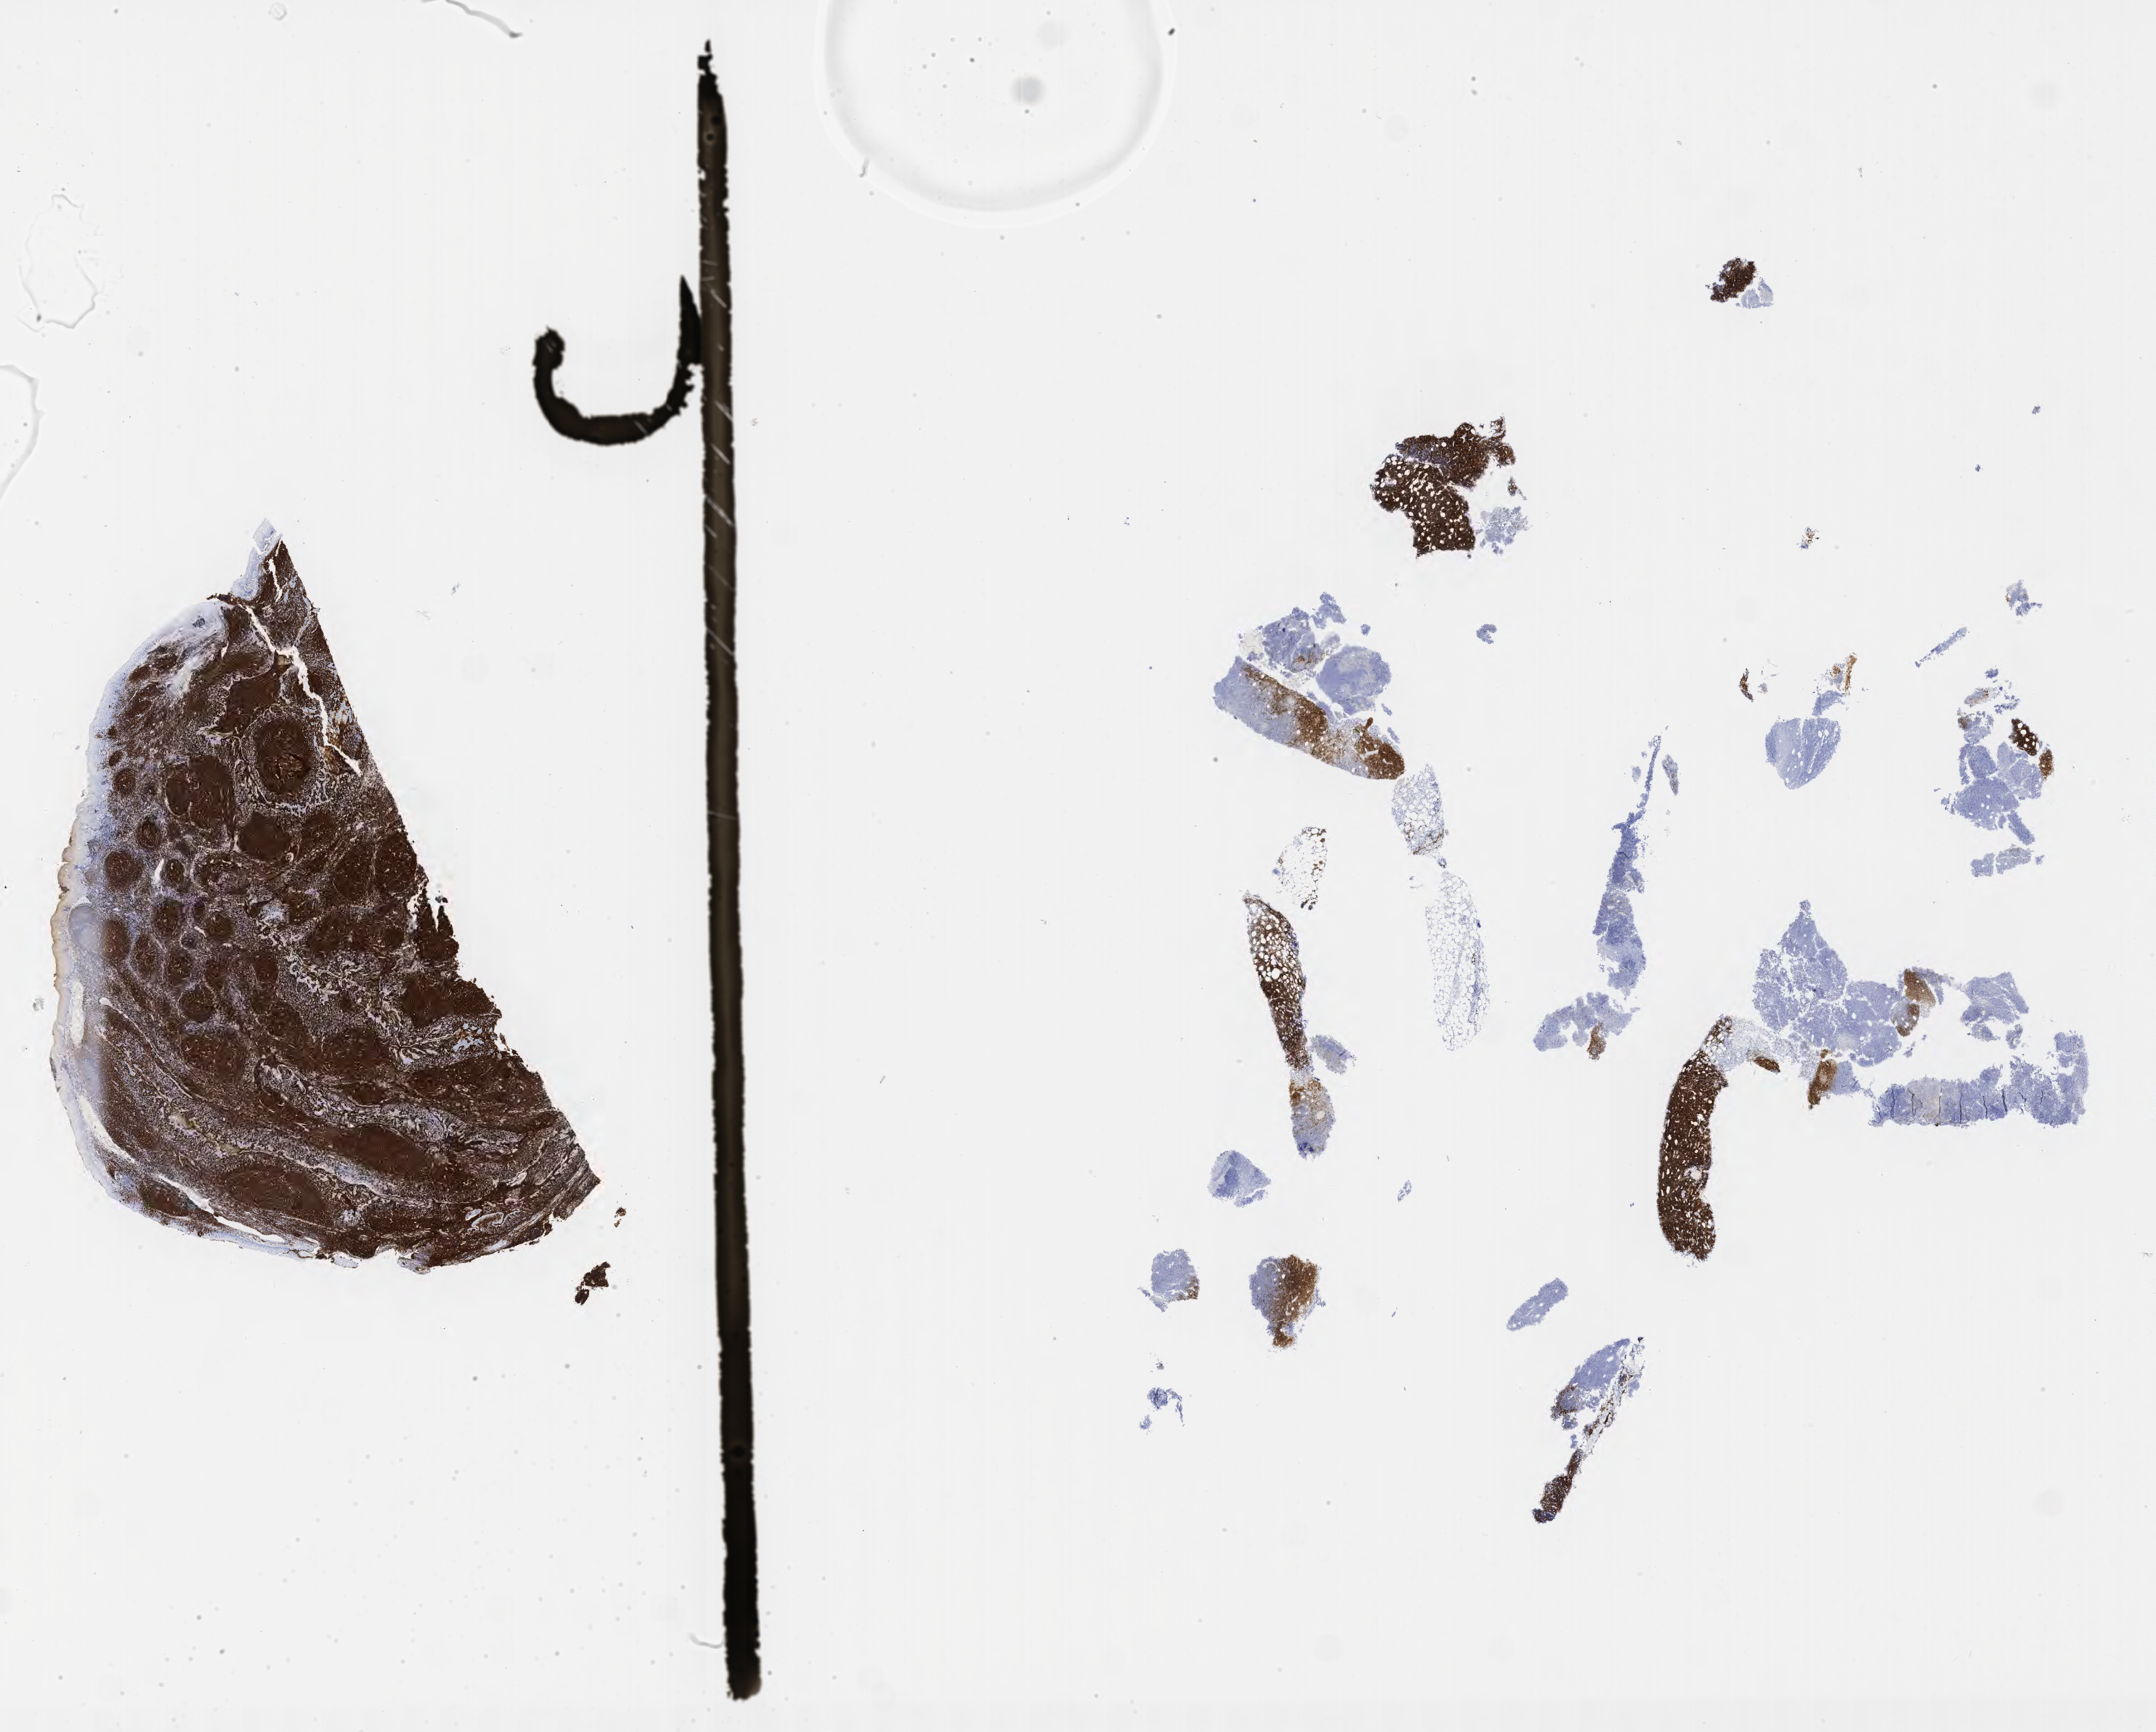
Whole-slide image, immunohistochemical stain for CD20 — a low-resolution overview of the entire scanned area, about 27.7 x 22.2 mm, tumor tissue, anatomic site: pelvis. Patient: female, aged 64.
Diagnosis: Burkitt lymphoma, NOS.